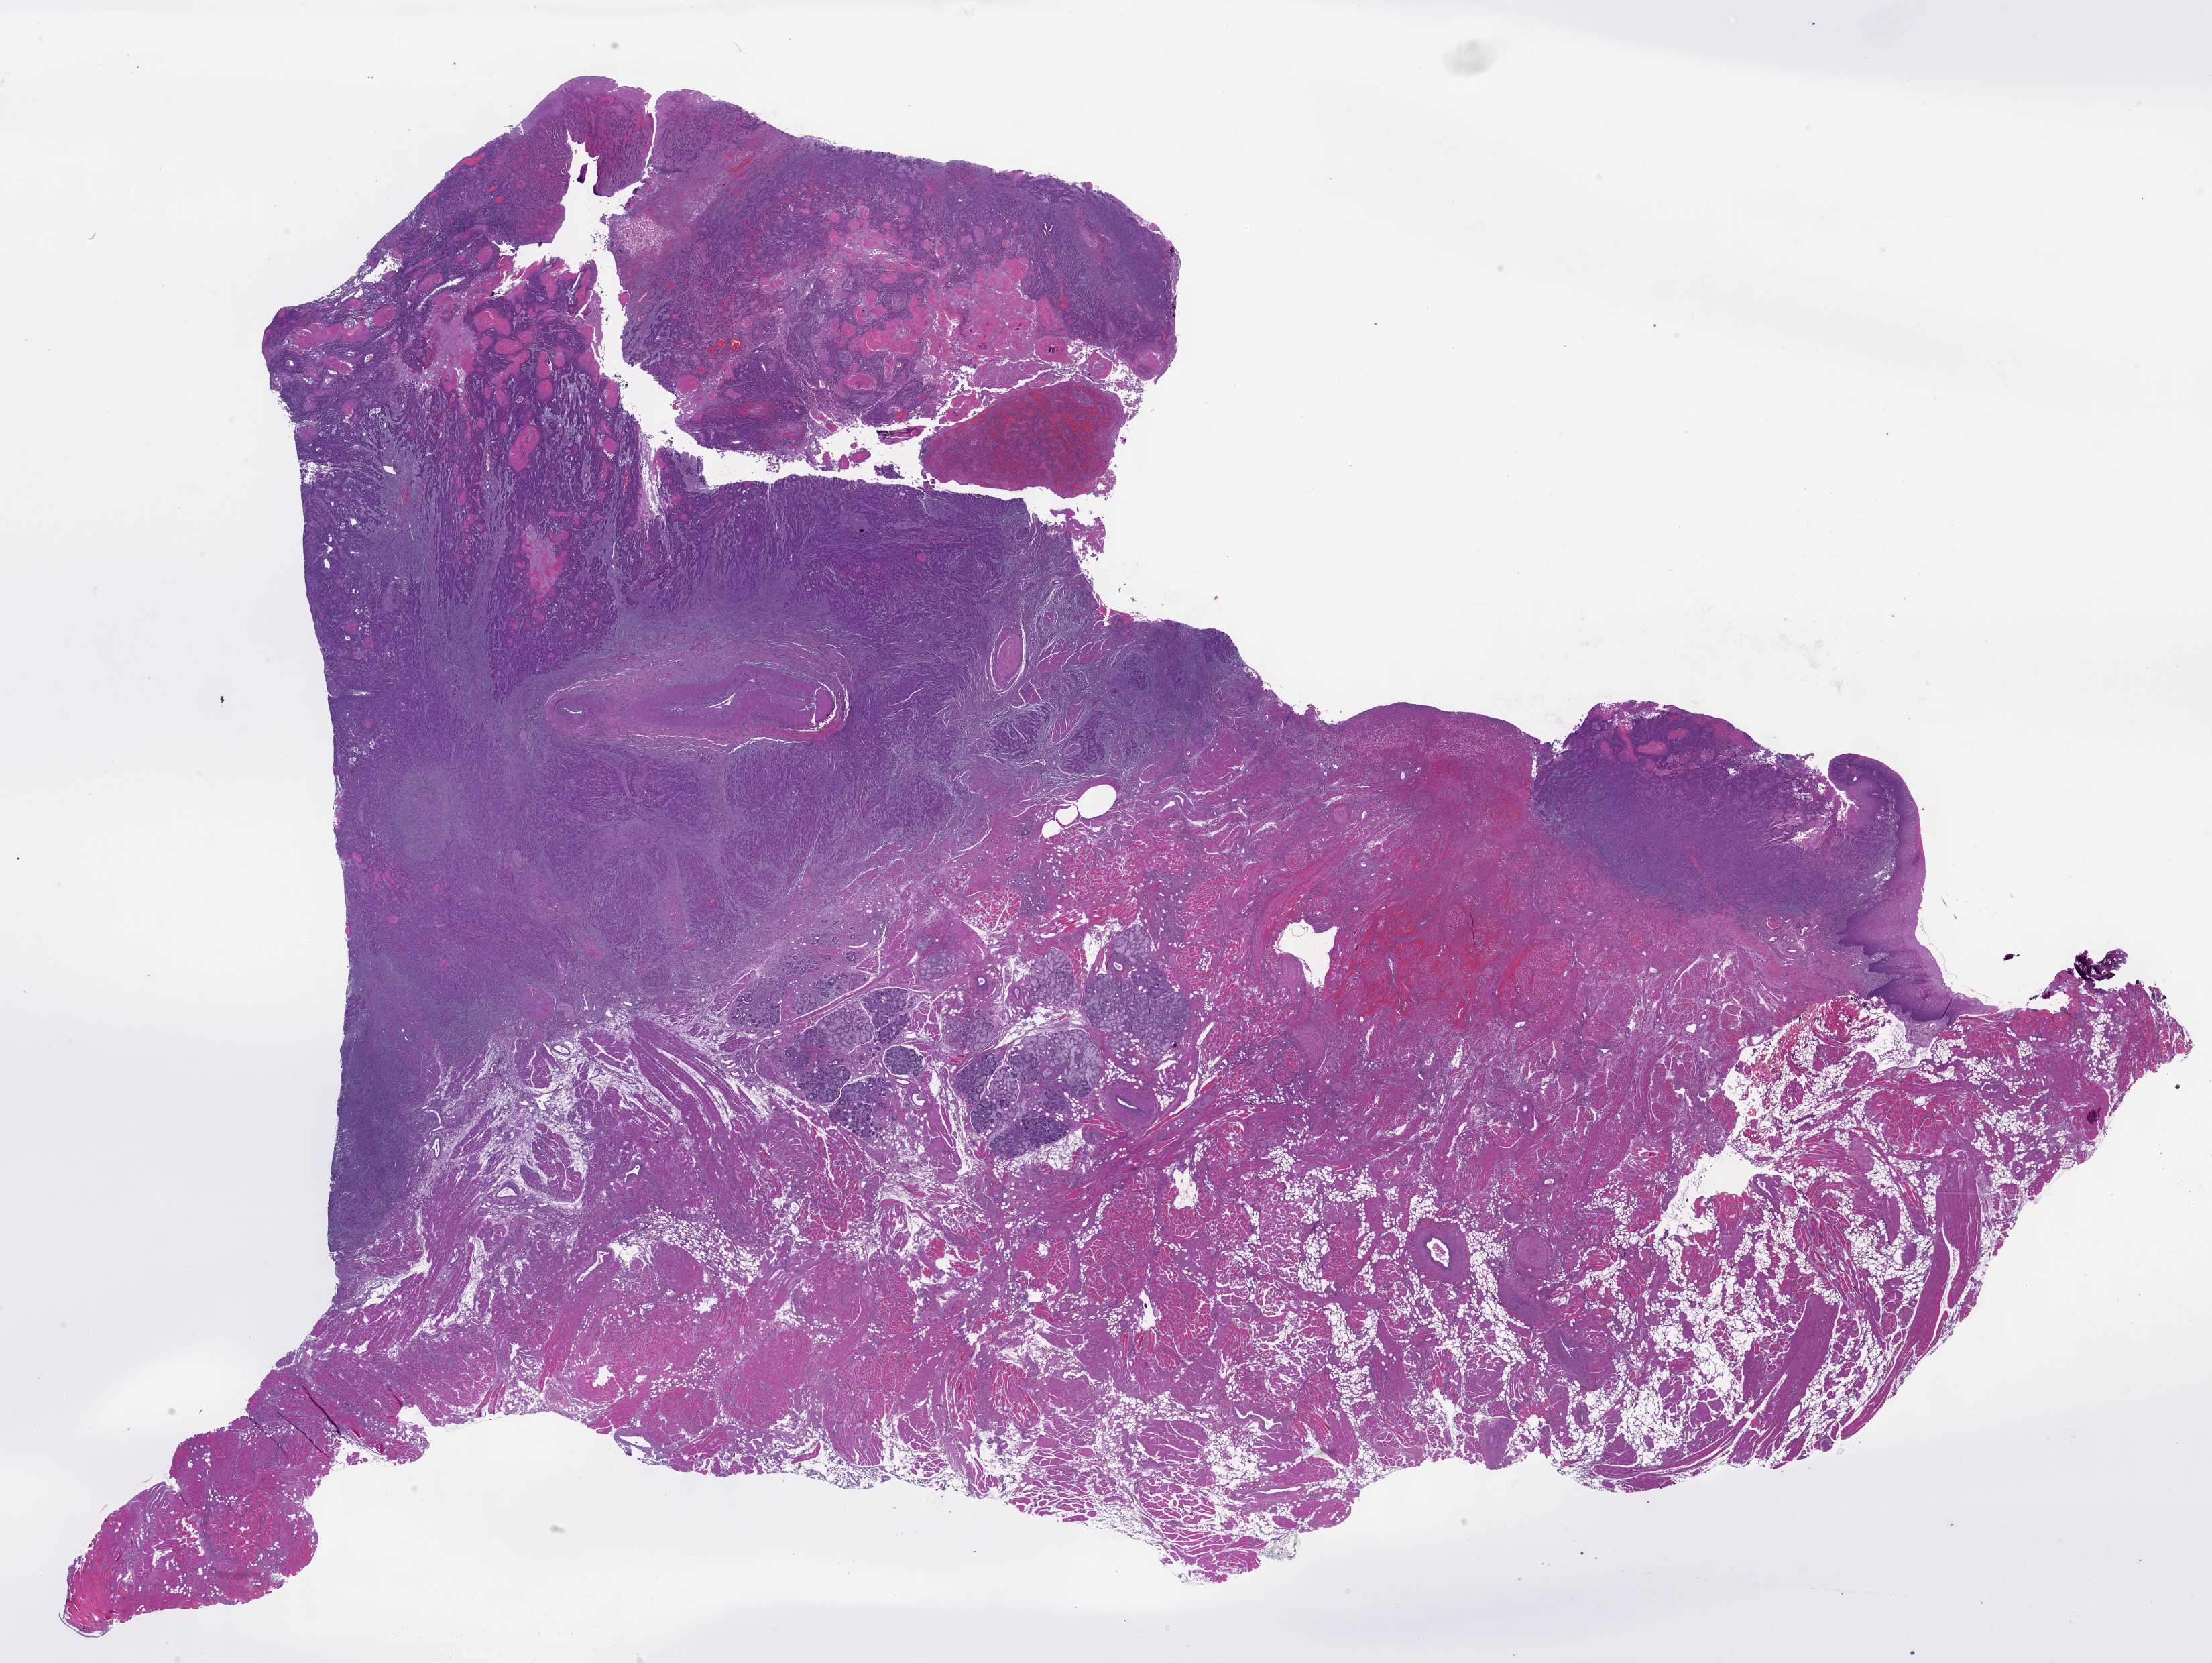
H&E whole-slide image — whole scanned area (about 26.7 x 20.0 mm, from a 40x scan) shown as a low-resolution overview. Formalin-fixed paraffin-embedded (FFPE) diagnostic section. Primary tumour sample from the head and neck. Male patient; age at initial diagnosis 65 years. Histologic grade: G2 (moderately differentiated).
• AJCC pathologic stage: IVA (7th edition)
• pathologic diagnosis: Squamous cell carcinoma, NOS (floor of mouth, NOS)